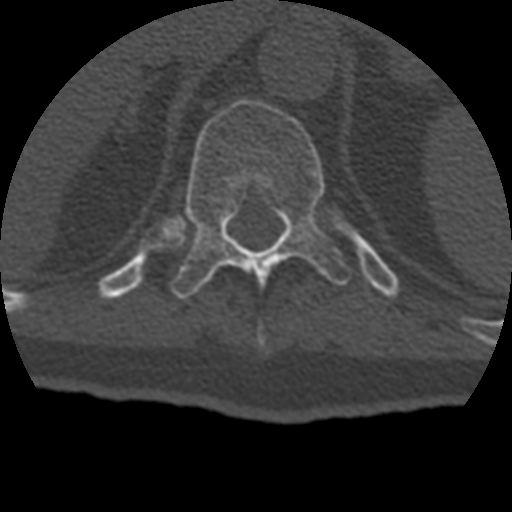
CT including the spine, one axial slice. Slice 199 of 399 in the series (ordered by position). Bone window (W 1800 / L 400 HU). 1.25 mm slice thickness. 512 × 512 image matrix, field of view 160 × 160 mm. Patient age 69 years. Case-level facts recorded for this patient, not image findings: primary cancer: prostate.
Structures marked on this image (semi-automatically segmented with operator editing):
- T11 vertebra: box from (x=171, y=99) to (x=352, y=299) px